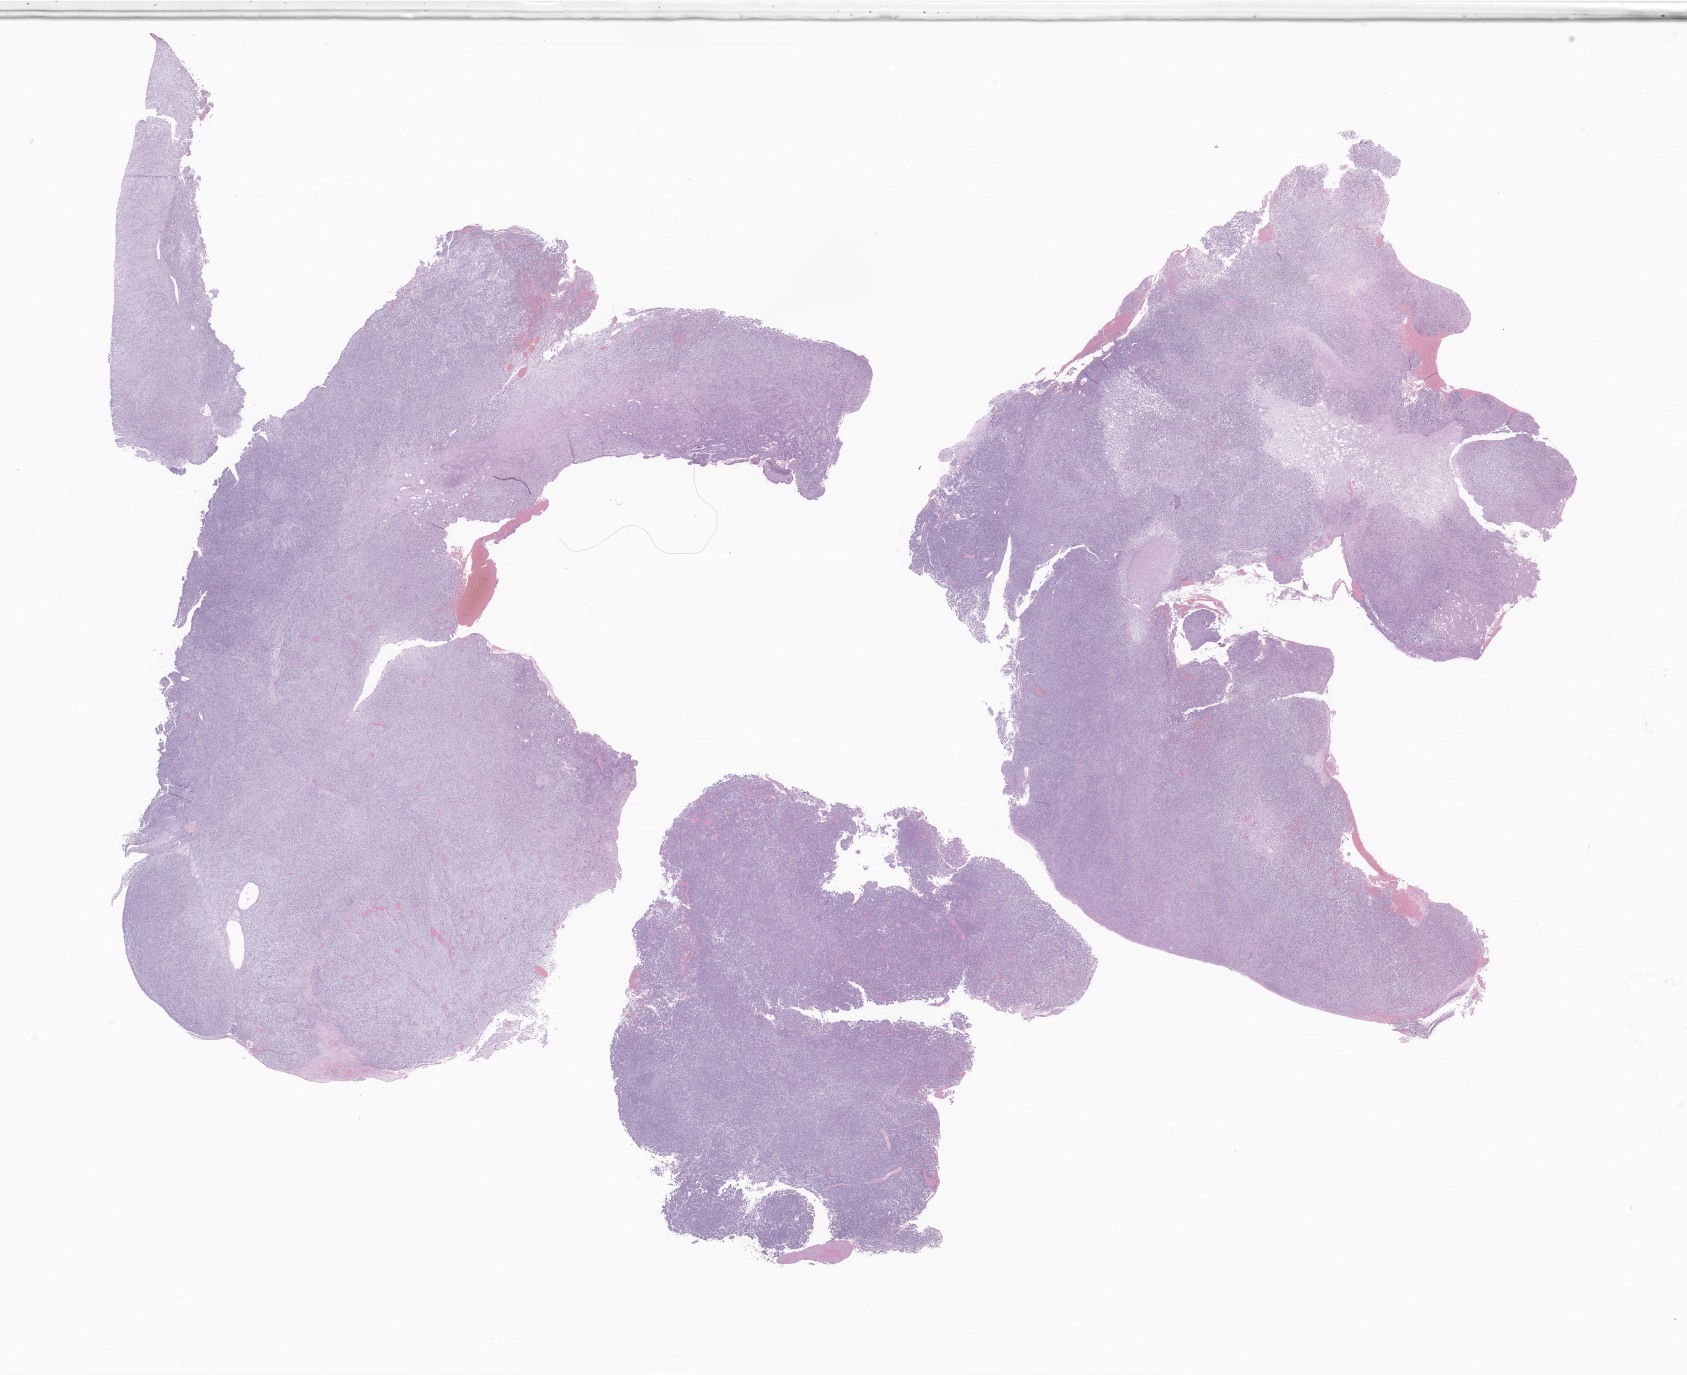
Digitized H&E-stained section of tumor tissue from the cerebellum — whole scanned area (about 28.4 x 23.2 mm) shown as a low-resolution overview; formalin-fixed paraffin-embedded section. Patient male; age 434 days (about 1.2 years).
• diagnosis: Atypical teratoid/rhabdoid tumor